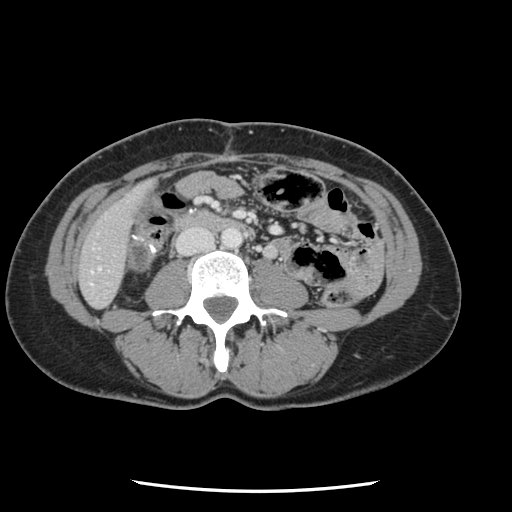
Contrast-enhanced abdominal CT, one axial slice. Position 14 of 134 along the scan axis. Intravenous contrast given. Soft-tissue window (W 400 / L 40 HU). 2.5 mm slice thickness. 512 × 512 image matrix, field of view 330 × 330 mm. Female patient, age 43 years. From the clinical record (not read from this slice): diagnosis: colorectal cancer liver metastases, imaged before liver resection; multiple liver metastases: yes; largest metastasis: 3.4 cm; disease in both lobes: yes.
Outlined on this slice (outlined manually by an expert reader):
- liver: bounding box (x1, y1, x2, y2) in pixels: (80, 187, 145, 307)
- planned liver remnant (the part of the liver to remain after resection): (80, 187, 146, 308)